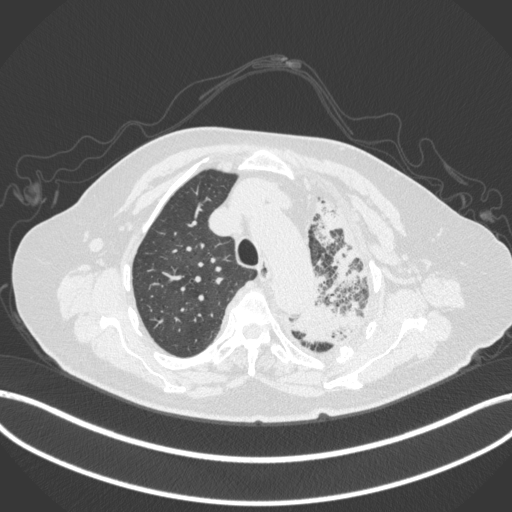
Chest CT, one axial slice. Position 302 of 399 along the scan axis. Lung window (W 1500 / L -600 HU). 512 × 512 image matrix, field of view 400 × 400 mm. Female patient, age 75 years. Case-level facts recorded for this patient, not image findings: clinical TNM (as recorded): T3 N3 M1.
Outlined on this slice (bounding box drawn by a radiologist):
- lung tumour (recorded histology: adenocarcinoma): bounding box <289,201,366,353> (left, top, right, bottom; pixels)